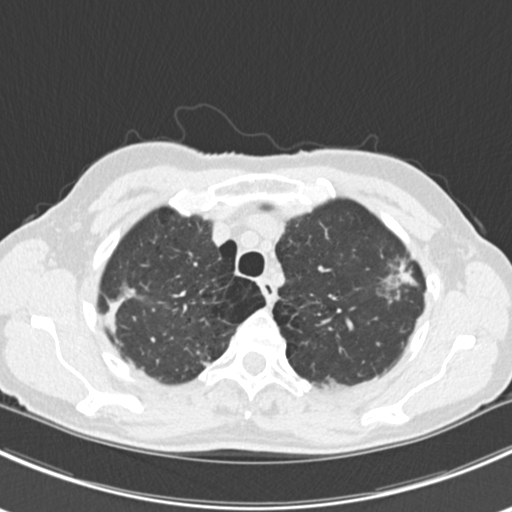
Low-dose screening chest CT, axial slice. Baseline screening round. Lung window (W 1500 / L -600 HU). Slice 39 of 224 in the series. 512 × 512 image matrix. Female participant, aged 63 years at enrolment. Current smoker at enrolment.
• Expert reader's lesion annotation, bounding box (x1, y1, x2, y2) in pixels: (365, 250, 428, 313).
• The screening reader recorded 10 non-calcified nodules or masses ≥4 mm on this exam (right lower lobe, right lower lobe, left lower lobe, left lower lobe, right middle lobe, right lower lobe, left lower lobe, left upper lobe, right upper lobe, left upper lobe); which of them this box marks is not recorded.
• Official screen result: positive, change unspecified: nodule(s) >= 4 mm or enlarging nodule(s), mass(es), or other non-specific abnormalities suspicious for lung cancer.
• Lung cancer was diagnosed 751 days after this screen: bronchiolo-alveolar adenocarcinoma, NOS, right upper lobe, right middle lobe, right lower lobe, left upper lobe, left lower lobe, moderately differentiated (G2), stage IV (AJCC 6th edition).